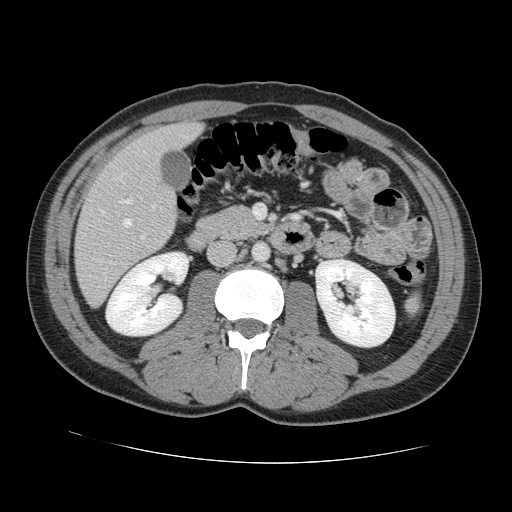
Contrast-enhanced abdominal CT, one axial slice; position 50 of 131 along the scan axis; 120 kVp; intravenous contrast given; soft-tissue window (W 400 / L 40 HU); 512 × 512 image matrix, field of view 380 × 380 mm. Male patient, age 40 years. Case-level facts recorded for this patient, not image findings: diagnosis: colorectal cancer liver metastases, imaged before liver resection; multiple liver metastases: yes; largest metastasis: 2.9 cm.
Outlined on this slice (outlined manually by an expert reader):
- hepatic veins: bounding box (x1, y1, x2, y2) in pixels: (102, 211, 131, 227)
- liver: (76, 124, 201, 305)
- planned liver remnant (the part of the liver to remain after resection): (121, 124, 201, 169)
- portal vein (with intrahepatic branches): (120, 198, 144, 239)